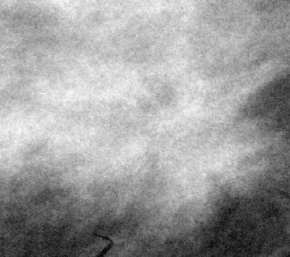
Cropped region of a digitized screen-film mammogram centred on a radiologist-marked abnormality, right breast, MLO view.
- Marked abnormality: mass, shape irregular, margins spiculated; BI-RADS assessment category 4; pathology (as recorded): malignant.